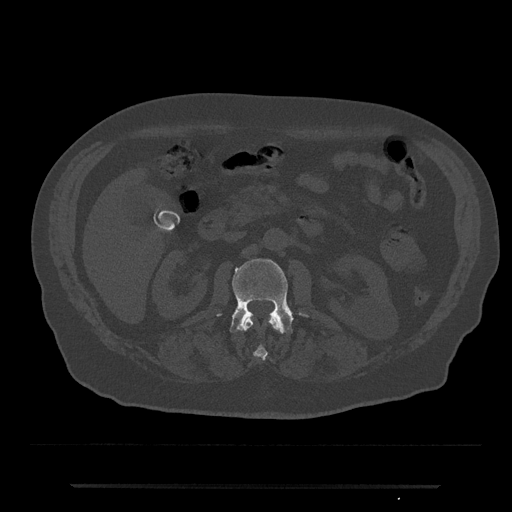
CT including the spine, one axial slice. Slice 490 of 797 in the series (ordered by position). Reconstruction kernel Br40s/3. 120 kVp. Bone window (W 1800 / L 400 HU). 0.5 mm slice thickness. 512 × 512 image matrix, field of view 434 × 434 mm. Patient: male, 80 years. From the clinical record (not read from this slice): primary cancer: prostate.
Structures marked on this image (semi-automatic segmentation, software-assisted and operator-edited):
- L1 vertebra: box from (x=242, y=316) to (x=282, y=360) px
- L2 vertebra: (x=217, y=259)–(x=309, y=334)